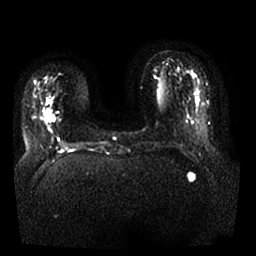
Breast MRI, one axial slice. Slice 5 of 25 in the series (ordered by position). Diffusion-weighted series; image 2 of 4 stored at this slice position (different b-values; order by instance number). 1.5 T. 4 mm slice thickness. 256 × 256 image matrix, field of view 350 × 350 mm. Female patient.
Structures marked on this image (expert manual segmentation):
- tumour on diffusion-weighted imaging: bounding box [x1, y1, x2, y2] px = [44, 109, 54, 121]